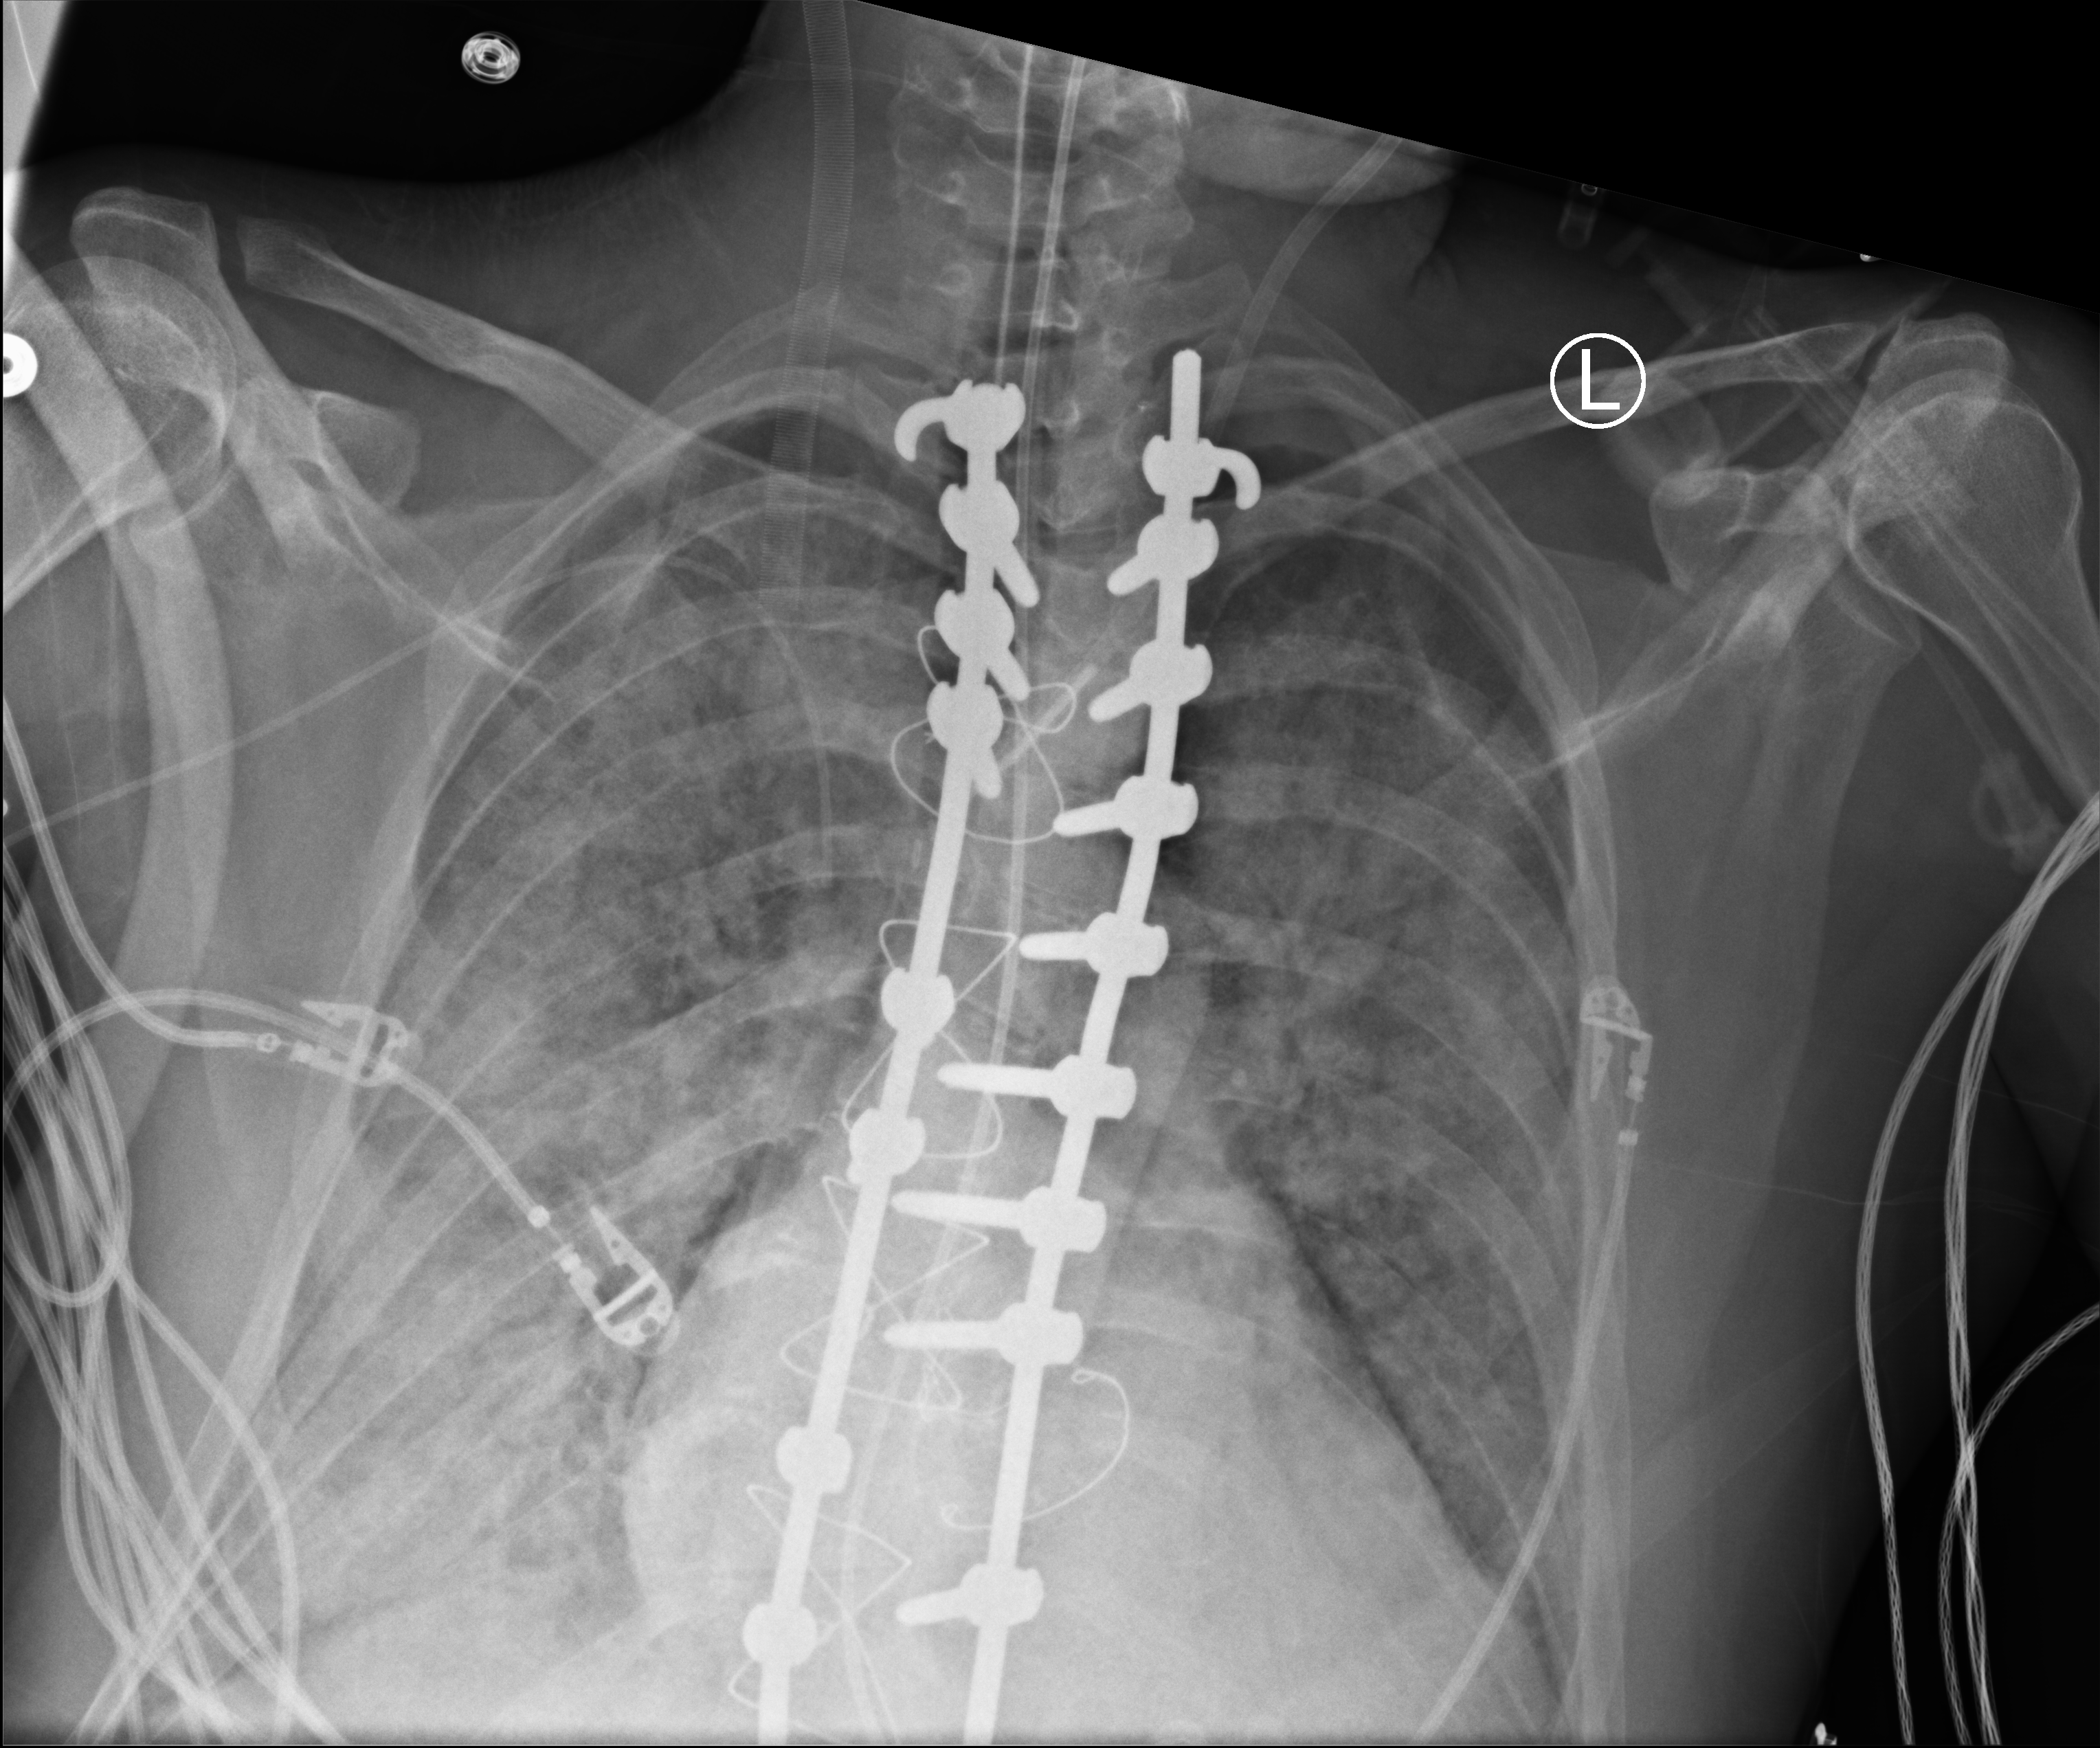
Chest X-ray (portable), anteroposterior (AP) projection. Patient hospitalised with COVID-19, aged 18–59 years.
Hospital-stay facts (about this admission, not read from this image; timing relative to this image not recorded): mechanically ventilated during this hospital stay: yes.